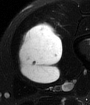
MRI of an extremity soft-tissue mass, one axial slice. Slice 23 of 65 in the series (ordered by position). T2-weighted fat-saturated. MR volume resampled by the dataset authors to the PET/CT grid (not the native acquisition matrix). 3.27 mm slice thickness. 90 × 105 image matrix. Male patient. Case-level facts recorded for this patient, not image findings: histological type: mixoid liposarcoma; grade: low; site of the primary tumour: left thigh.
Annotated regions visible in this slice (expert contour drawn on MRI and transferred to this co-registered scan by the dataset authors):
- gross tumour volume (mass): bounding box <18,21,63,83> (left, top, right, bottom; pixels)